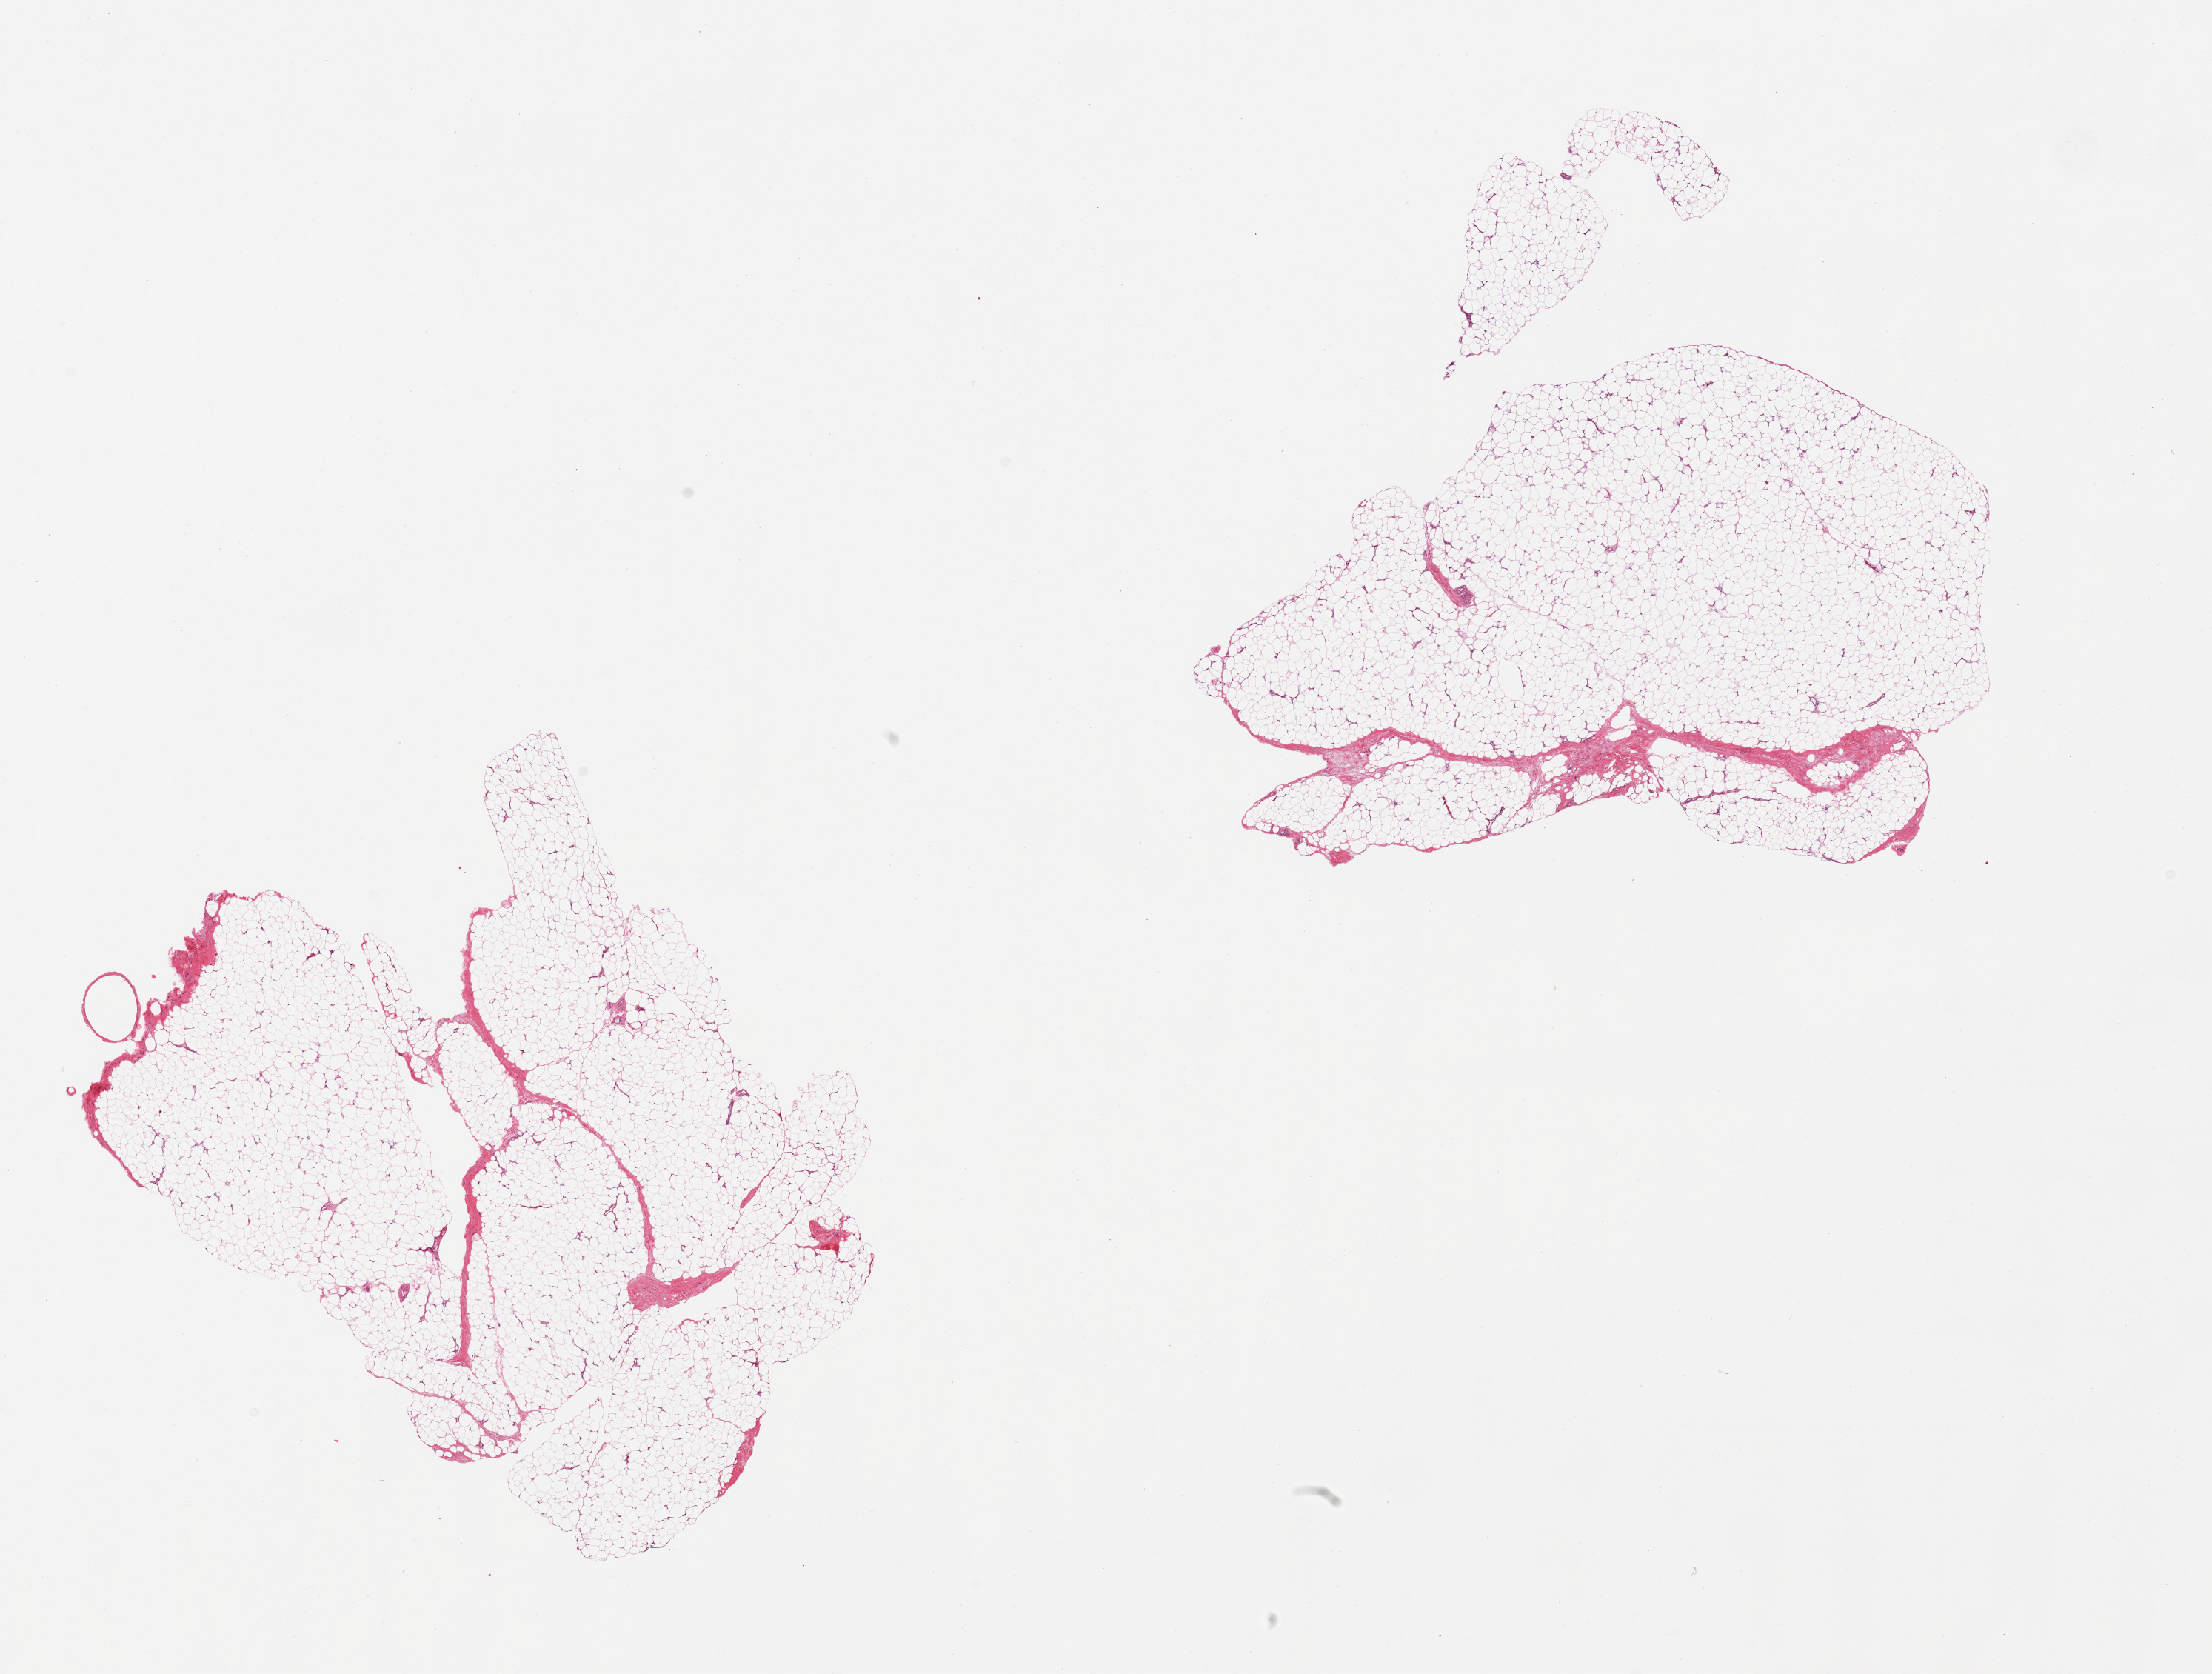
Hematoxylin and eosin (H&E) whole-slide image, brightfield, shown as a low-resolution overview of the whole scanned area (about 23.6 x 17.9 mm, slide scanned at 20x), PAXgene-fixed, paraffin-embedded tissue, target tissue: adipose tissue, donor tissue sample. Donor sex: male.
* pathologist's review note for this sample: 2 pieces